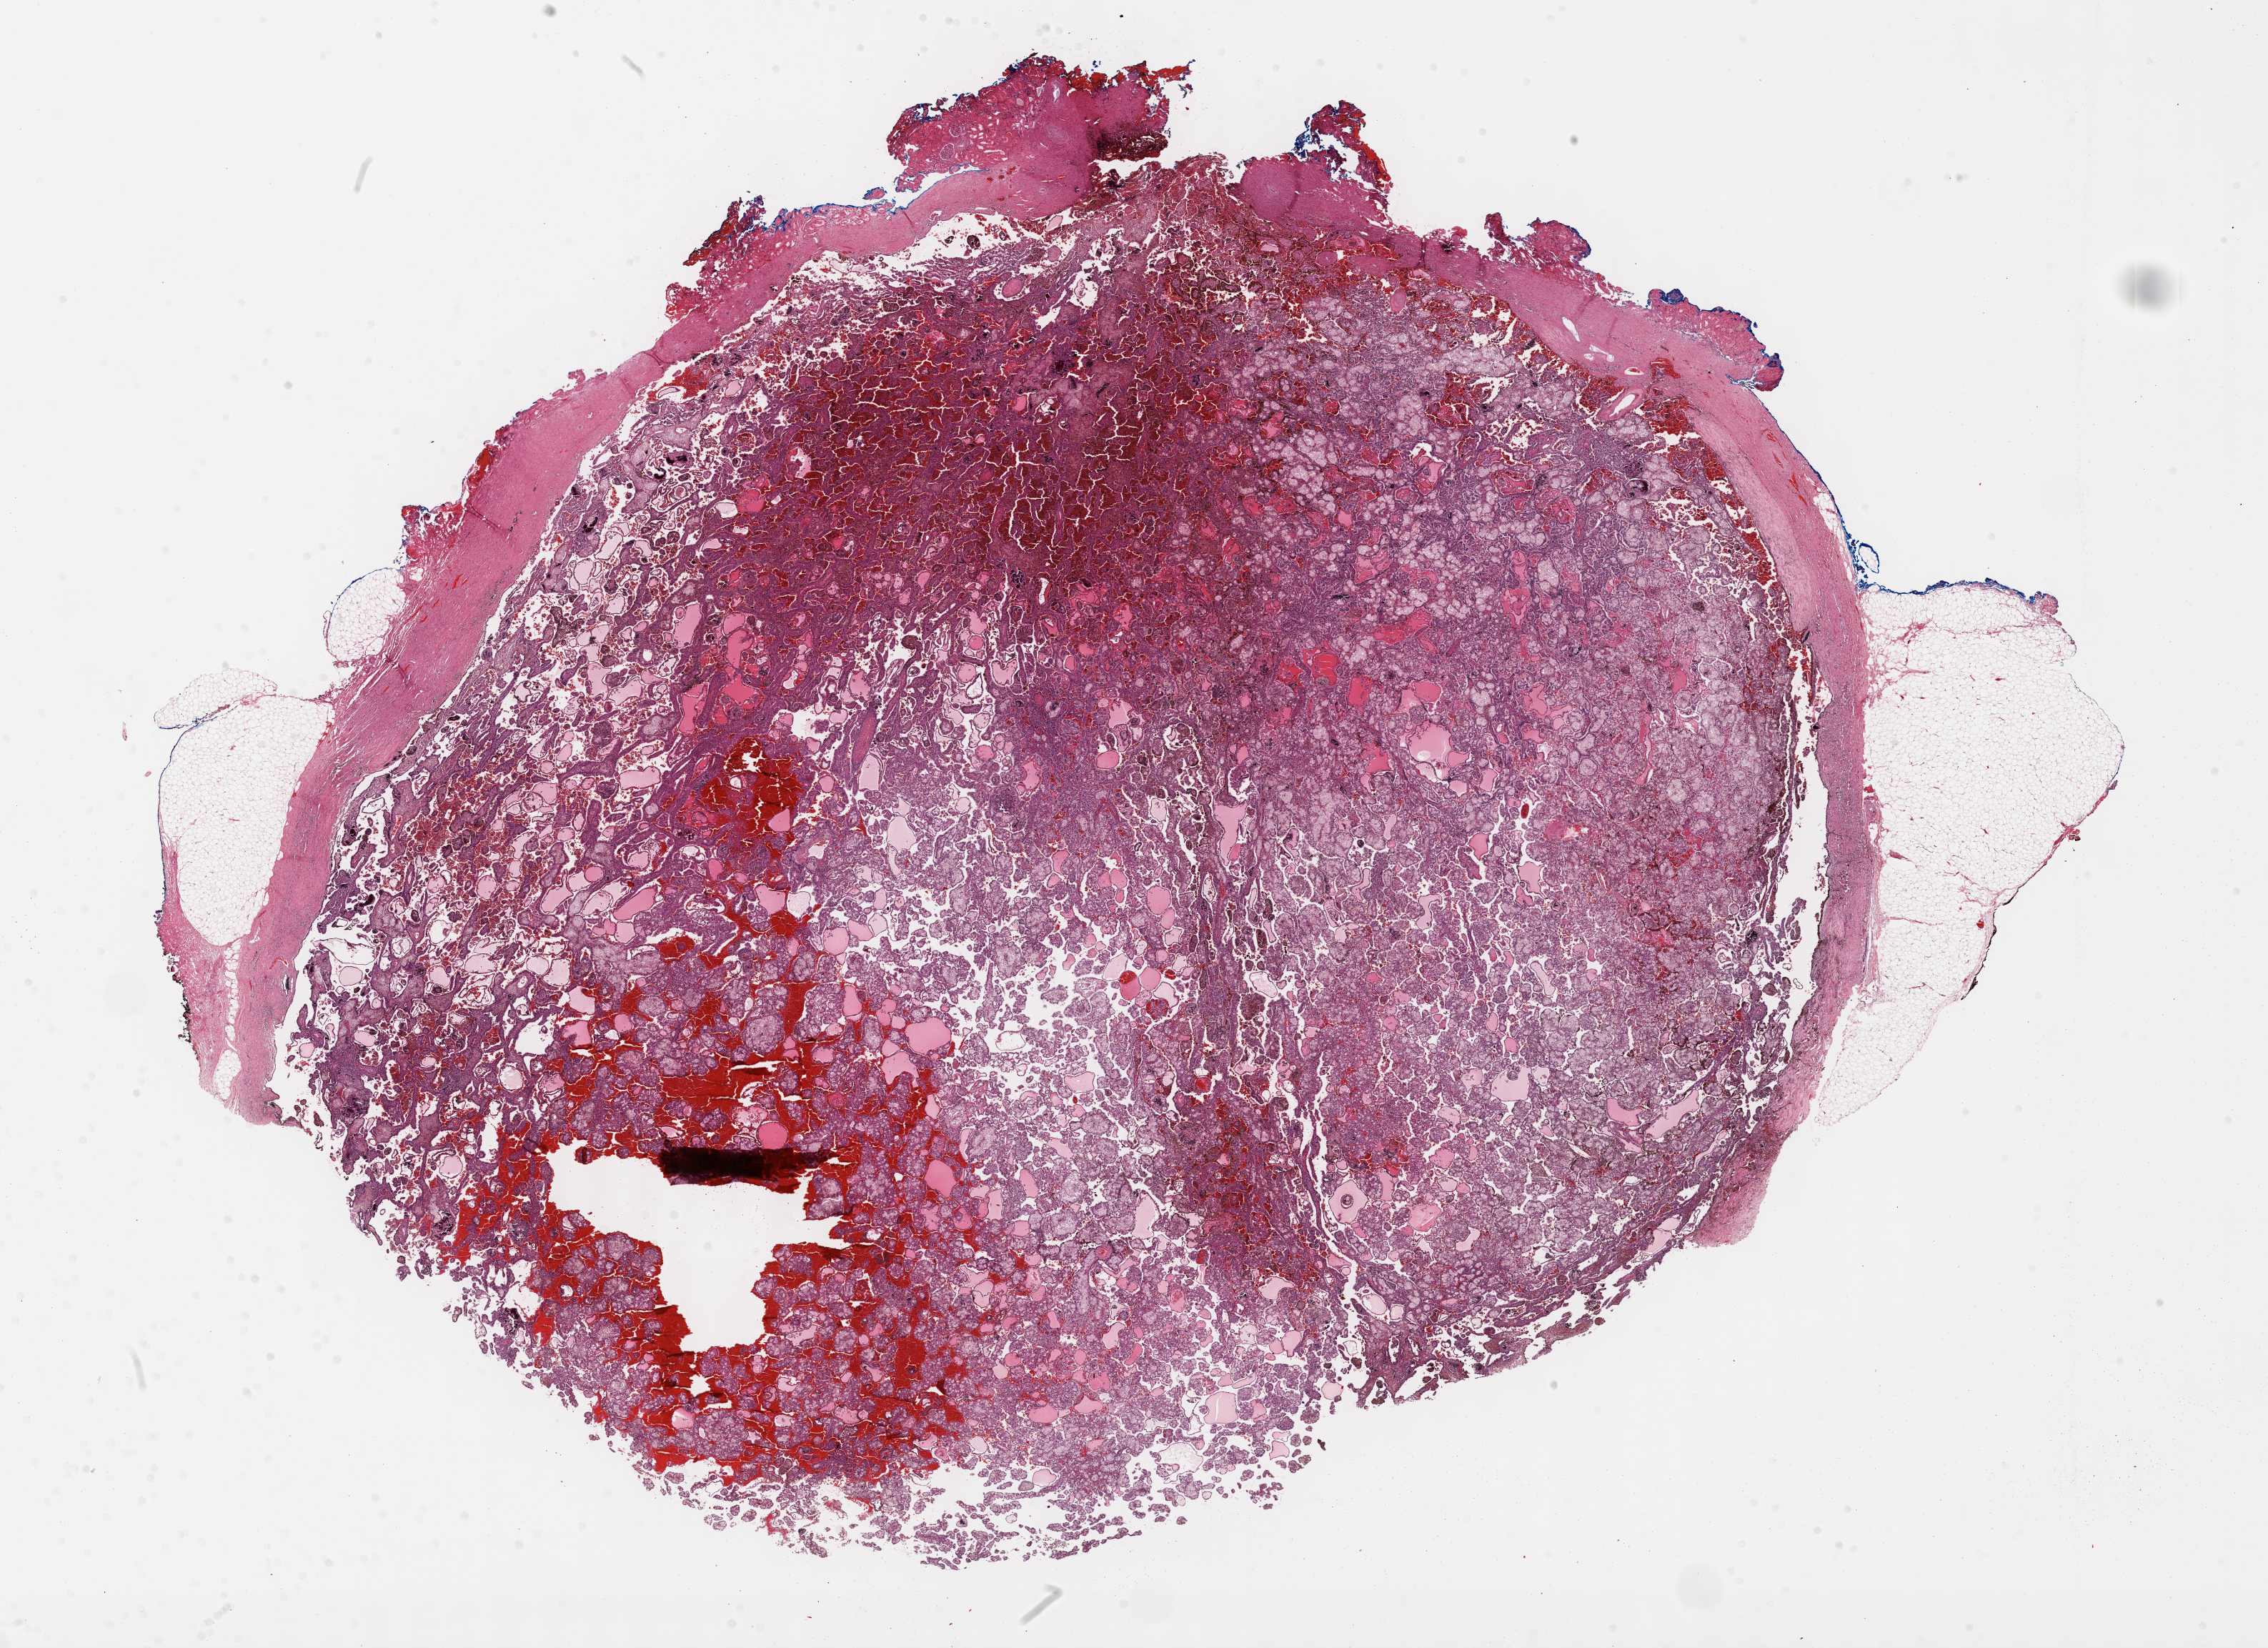
Hematoxylin and eosin (H&E) stained whole-slide image — a low-resolution overview of the entire scanned area, about 25.7 x 18.7 mm (from a 40x scan); formalin-fixed paraffin-embedded (FFPE) diagnostic section; kidney, primary tumour sample. Male, age 69 years at initial diagnosis.
Diagnosis: Papillary adenocarcinoma, NOS. AJCC pathologic stage: I (7th edition). Laterality: left.